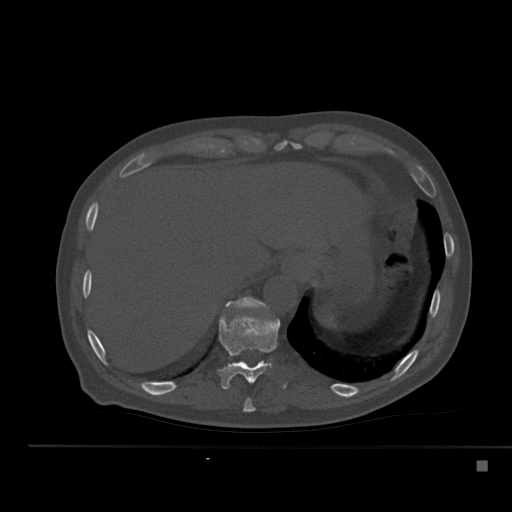
CT including the spine, one axial slice. Slice 267 of 517 in the series (ordered by position). Reconstruction kernel Br40s. Bone window (W 1800 / L 400 HU). 1.5 mm slice thickness. 512 × 512 image matrix. Patient: male, 70 years. Case-level facts recorded for this patient, not image findings: primary cancer: renal; vertebrae with lytic lesions (as recorded): T4, T6, T10, T12, L3, L4, L5.
Annotated regions visible in this slice (semi-automatic segmentation, software-assisted and operator-edited):
- T10 vertebra: box from (x=217, y=315) to (x=280, y=389) px
- T11 vertebra: (x=226, y=297)–(x=269, y=310)
- T9 vertebra: (x=243, y=398)–(x=256, y=412)